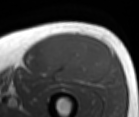
MRI of an extremity soft-tissue mass, one axial slice. Position 49 of 86 along the scan axis. MR volume resampled by the dataset authors to the PET/CT grid (not the native acquisition matrix). 3.27 mm slice thickness. 139 × 117 image matrix. Male patient. Case-level facts recorded for this patient, not image findings: histological type: extraskeletal osteosarcoma; grade: high; site of the primary tumour: thigh.
Annotated regions visible in this slice (expert contour drawn on MRI and transferred to this co-registered scan by the dataset authors):
- gross tumour volume (mass): box from (x=42, y=34) to (x=112, y=81) px